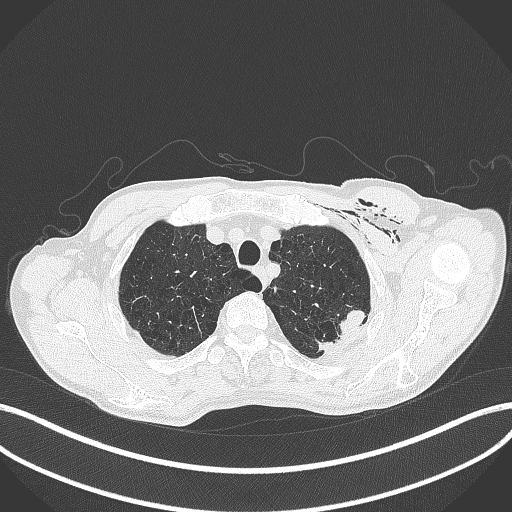
Chest CT, one axial slice; slice 354 of 457 in the series (ordered by position); reconstruction kernel B70f; 120 kVp; lung window (W 1500 / L -600 HU); 1 mm slice thickness; 512 × 512 image matrix, field of view 400 × 400 mm. Male patient, age 58 years. Case-level facts recorded for this patient, not image findings: clinical TNM (as recorded): T3 N0 M0.
Annotated regions visible in this slice (bounding box drawn by a radiologist):
- lung tumour (recorded histology: adenocarcinoma): bounding box [x1, y1, x2, y2] px = [315, 306, 371, 356]